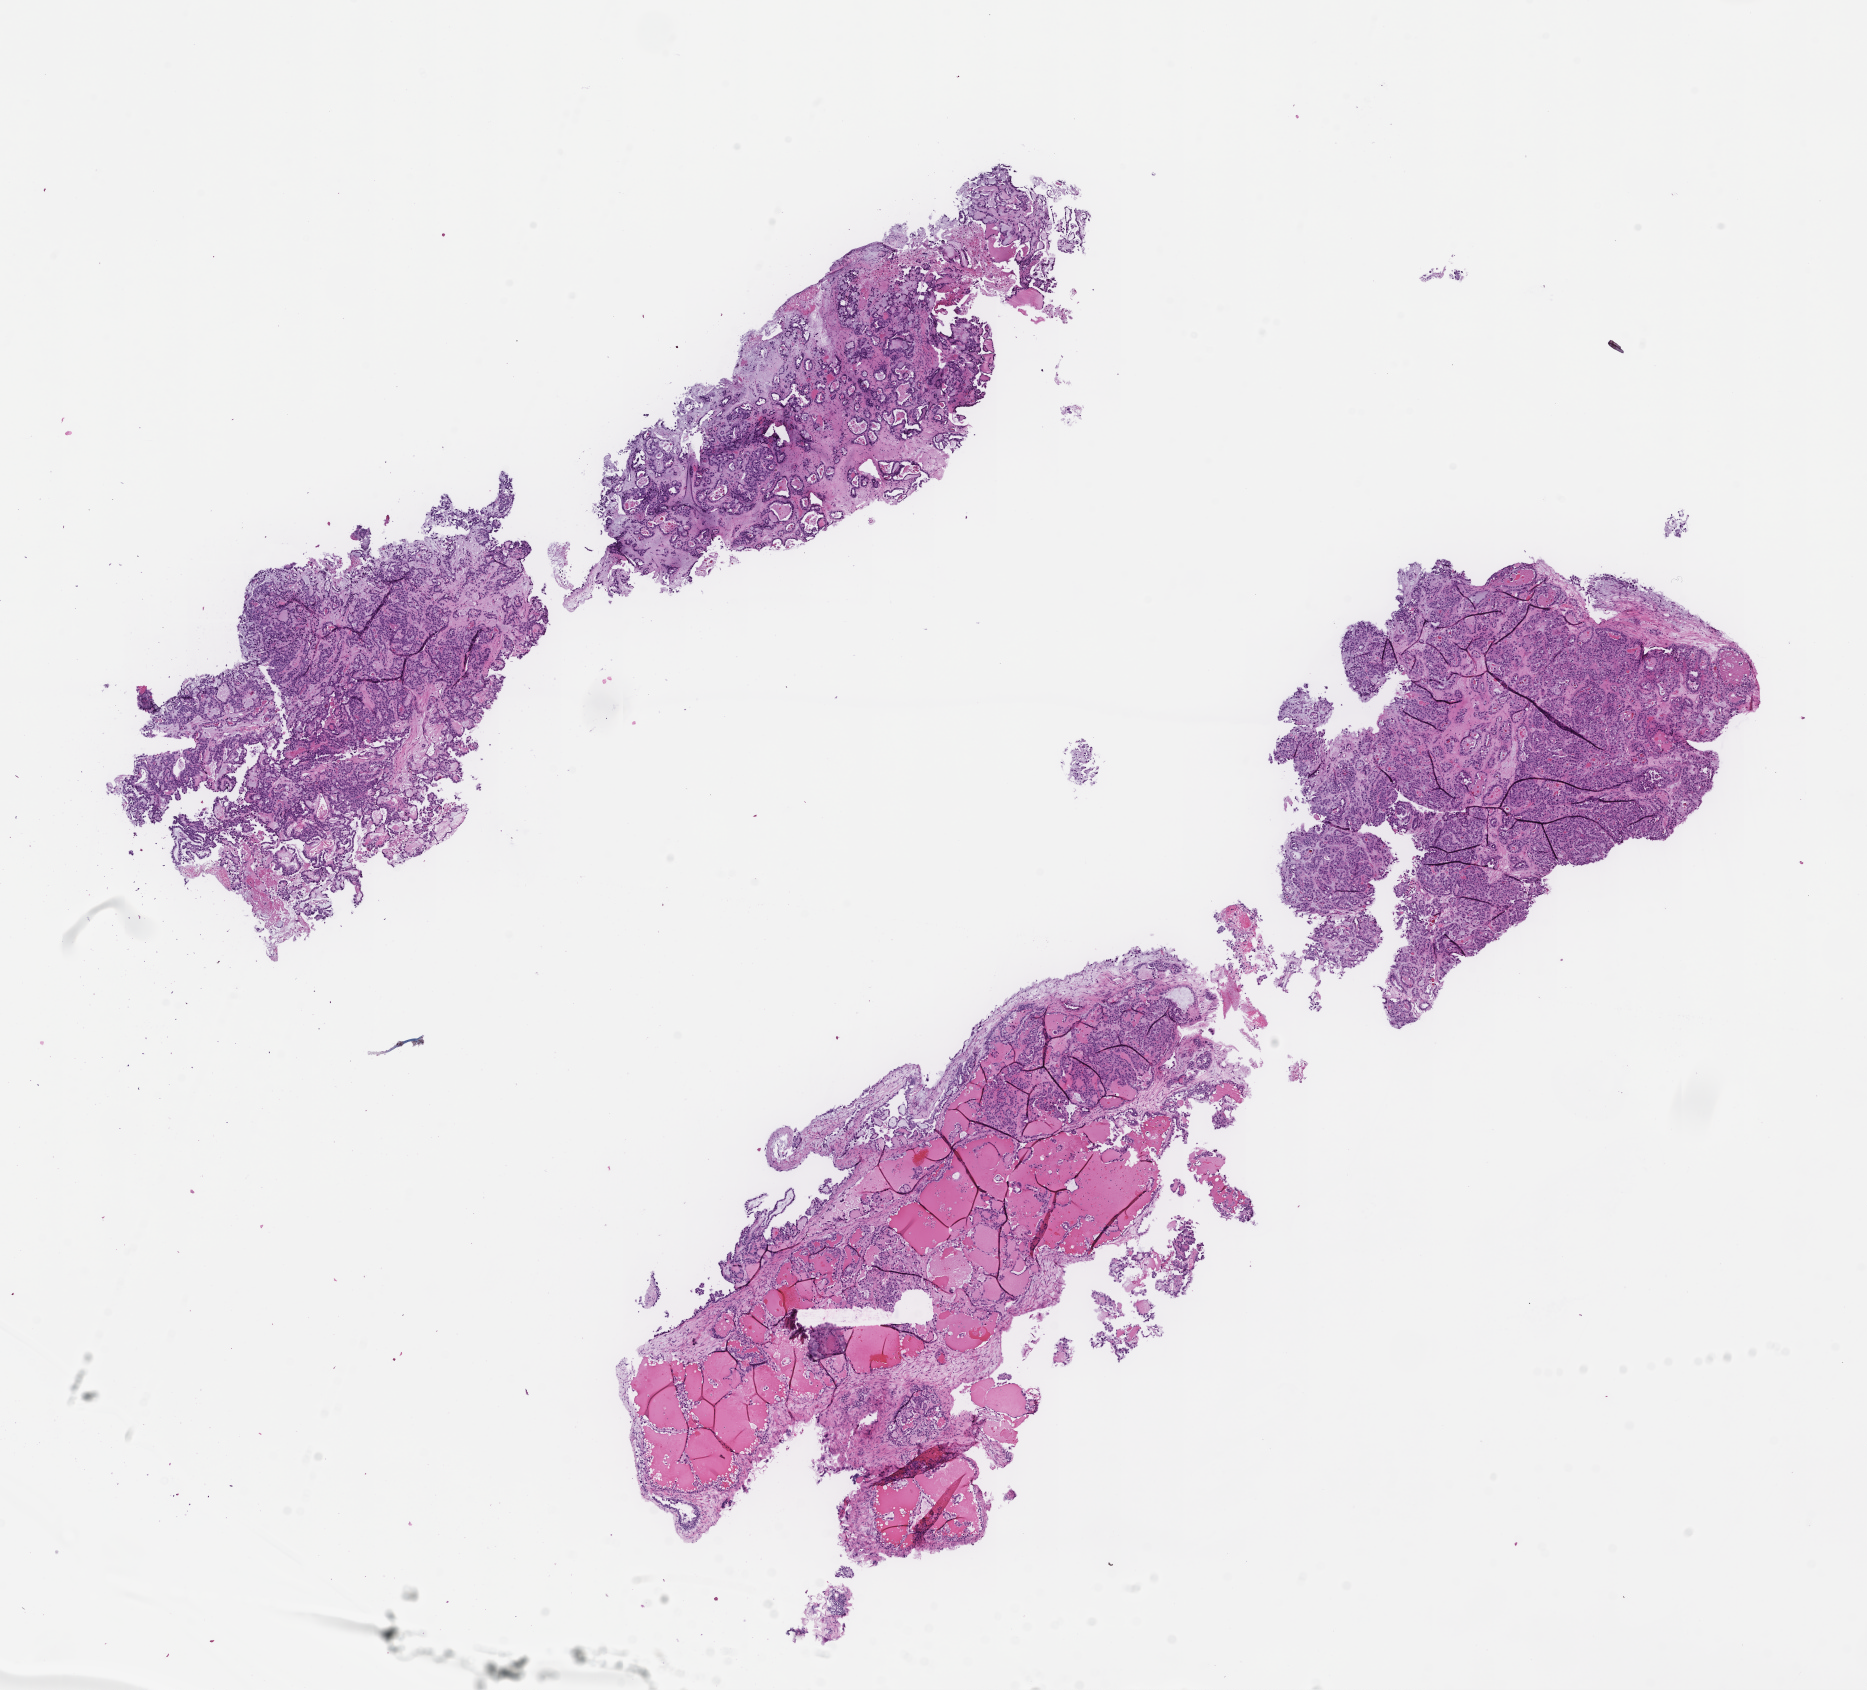
Digitized hematoxylin and eosin (H&E)-stained section — a low-resolution overview of the entire scanned area, about 15.1 x 13.6 mm, FFPE section, site: ovary, specimen time point: collected at baseline (before treatment). Patient: female.
This section: primary tumour tissue. Diagnosis: Ovarian Carcinoma.